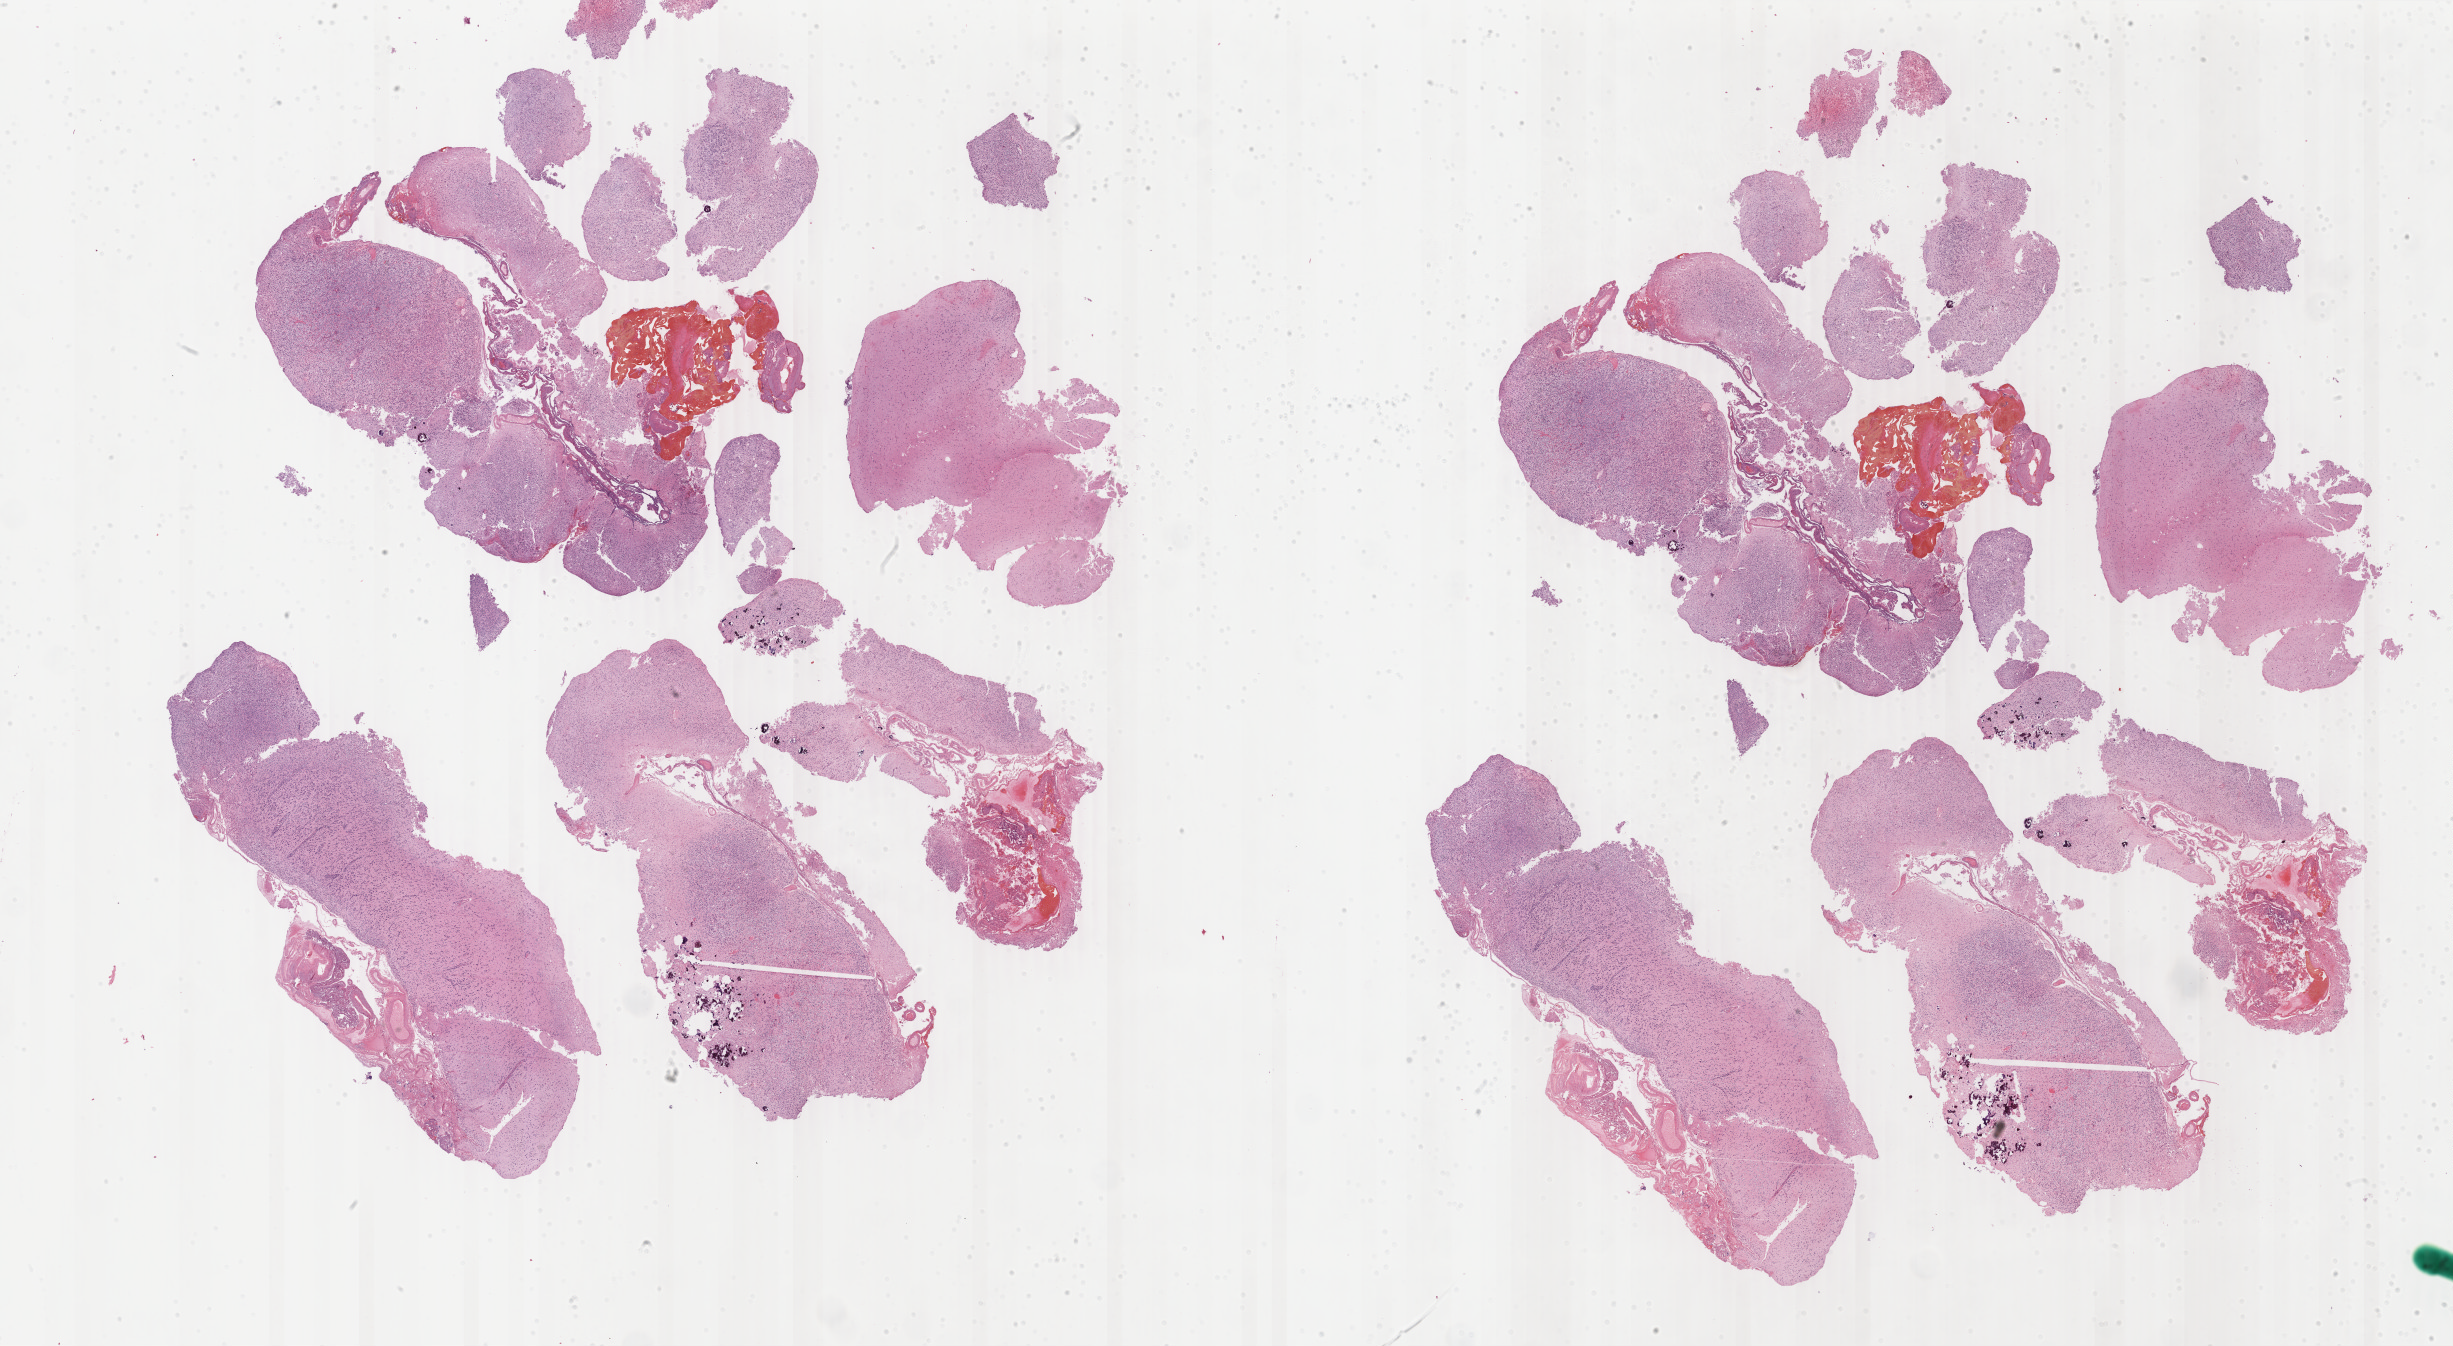
H&E whole-slide image, whole scanned area (about 39.0 x 21.4 mm) shown as a low-resolution overview, FFPE section, brain, primary tumour sample. Female patient; age at initial diagnosis 59 years. Histologic grade: G3 (poorly differentiated).
* pathologic diagnosis: Oligodendroglioma, anaplastic (cerebrum)
* laterality: right